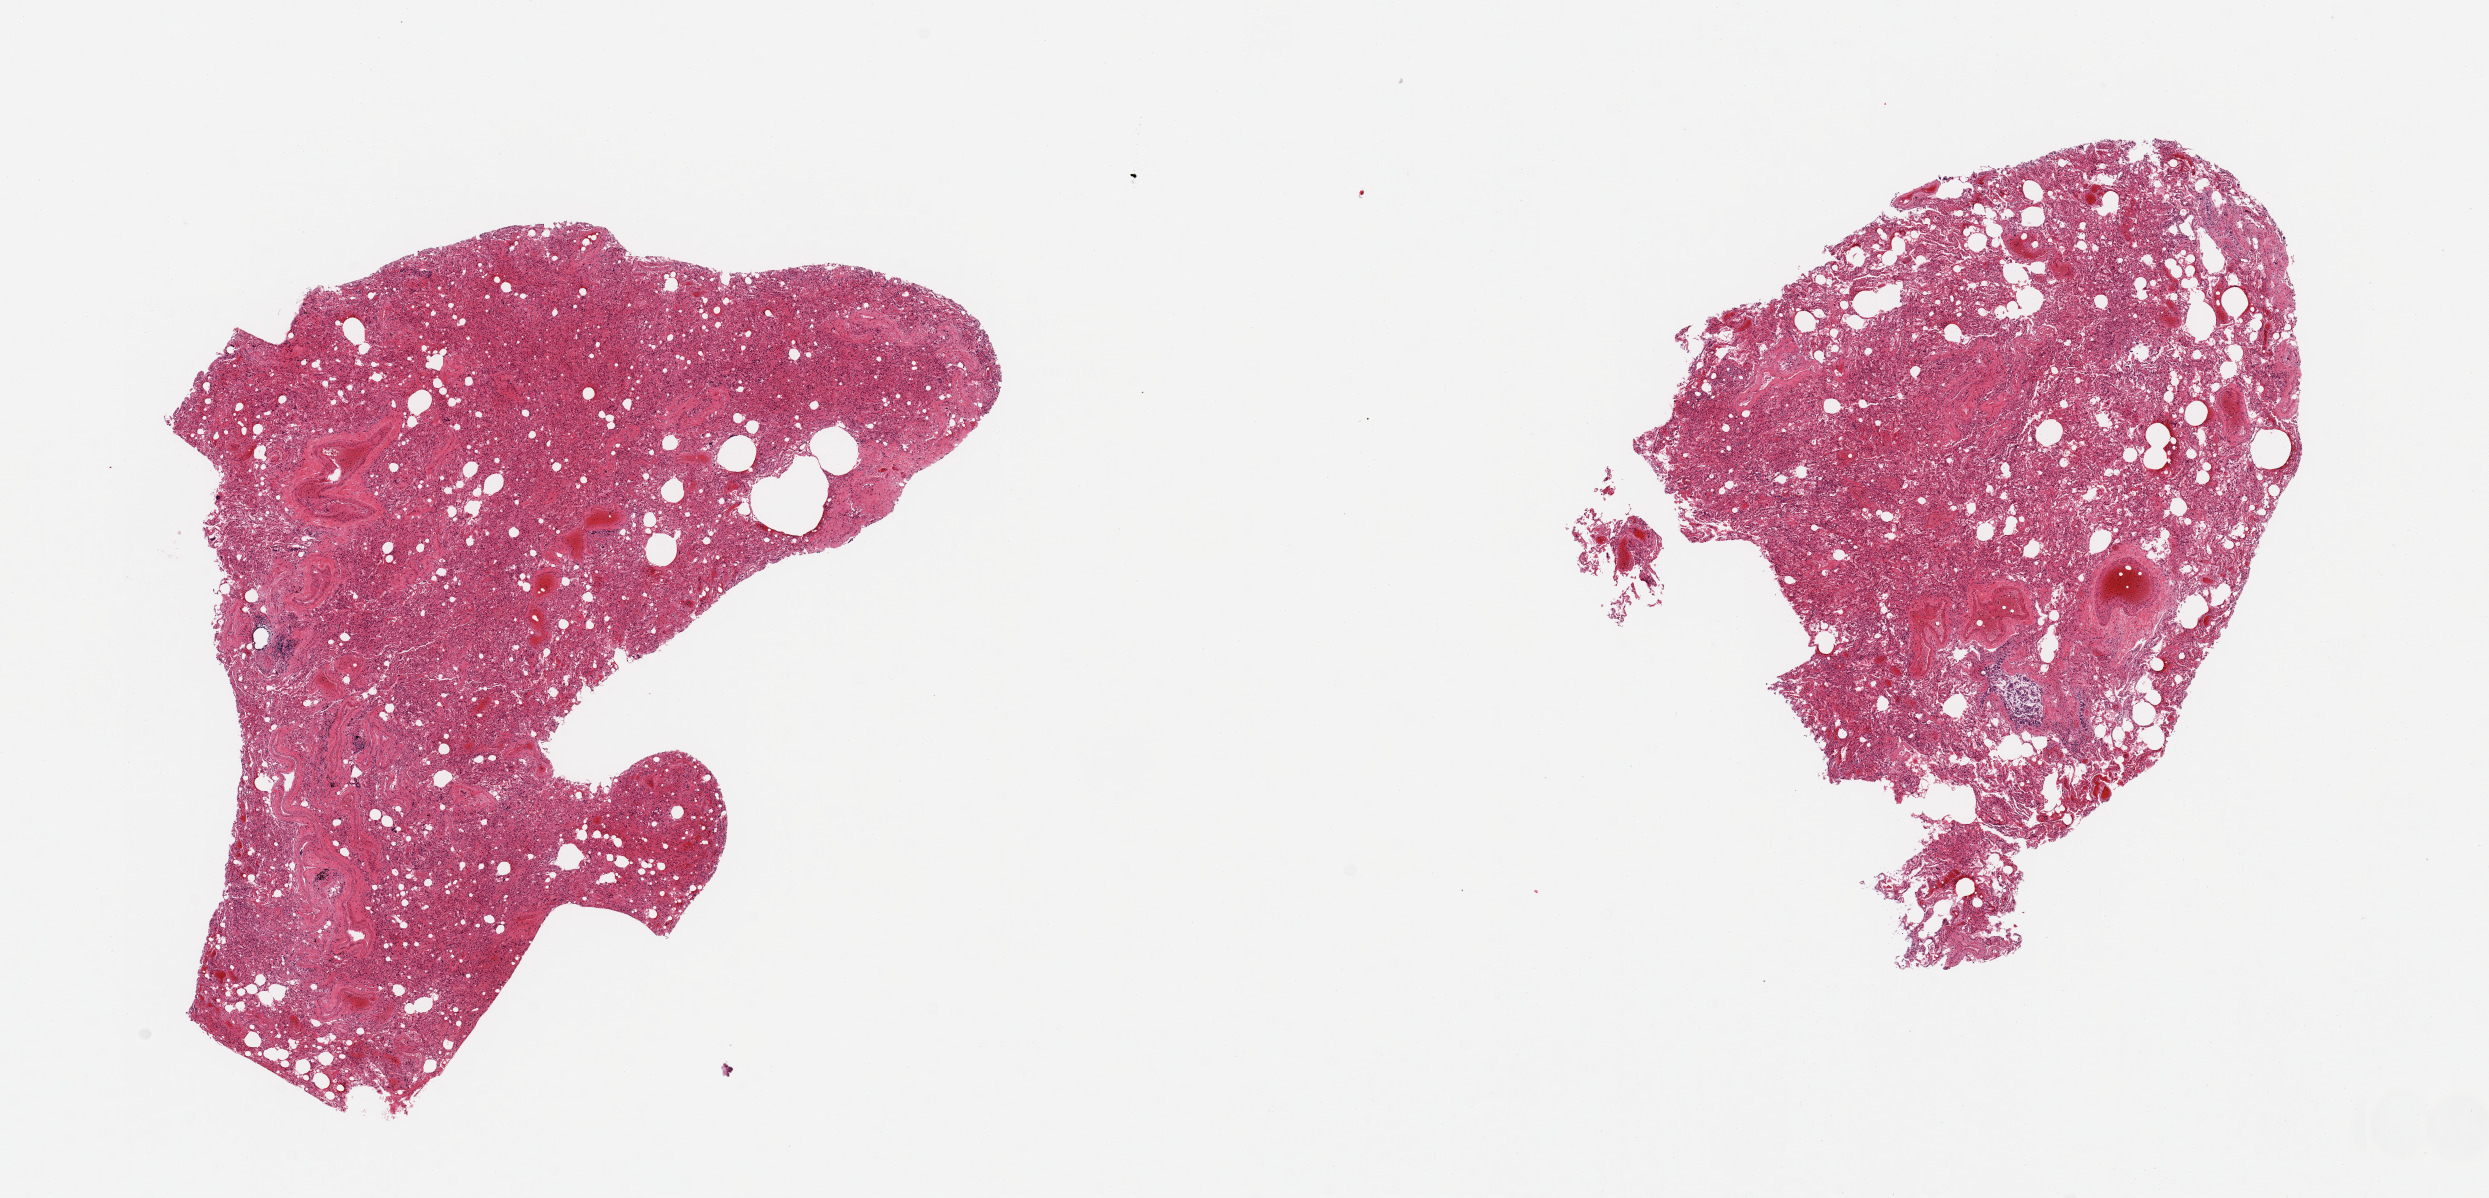
Digitized haematoxylin and eosin-stained section, whole scanned area (about 19.7 x 9.5 mm, from a 20x scan) shown as a low-resolution overview; PAXgene-fixed, paraffin-embedded tissue; sampled site (target tissue): lung; donor tissue sample. Donor sex: male.
Reviewer comment on this tissue sample: 2 pieces, advanced congestion; chronic pneumonitis, possible early fibrosis.